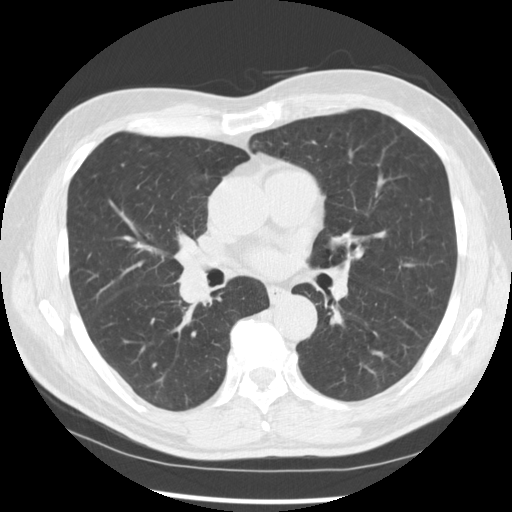
Low-dose screening chest CT, one axial slice. Slice 152 of 277 in the series (ordered by position). Reconstruction kernel STANDARD. 120 kVp. Lung window (W 1500 / L -600 HU). 2.5 mm slice thickness. 512 × 512 image matrix, field of view 365 × 365 mm.
Outlined on this slice (manually delineated by an expert):
- lesion 1 (tumor, middle lobe of right lung): bounding box [x1, y1, x2, y2] px = [179, 268, 212, 305]